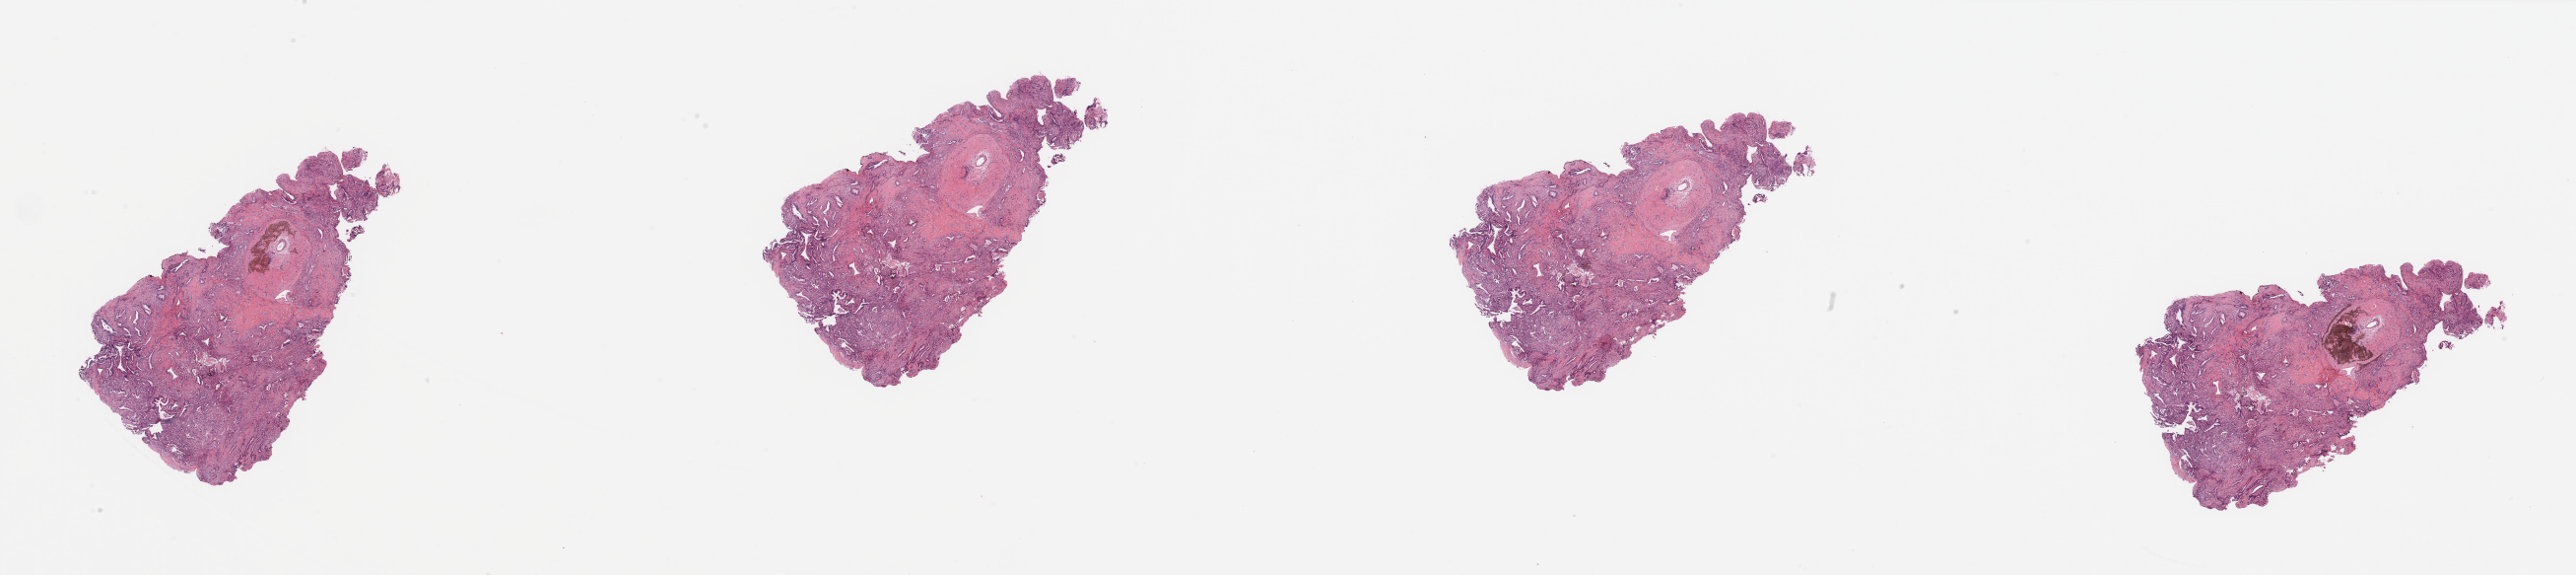
Digitized Hematoxylin and eosin (H&E) stained tissue section (whole slide) — shown as a low-resolution overview of the whole scanned area (about 41.3 x 9.2 mm). Tumour tissue sample, sampled site: pancreas. 62-year-old male patient. Histologic grade: G2 (moderately differentiated). Pathologist review of this section (percent, as recorded): tumour nuclei 60%, necrosis 0%.
Primary tumour site (as recorded): head. Diagnosis: Infiltrating duct carcinoma, NOS. AJCC pathologic stage: IIB.